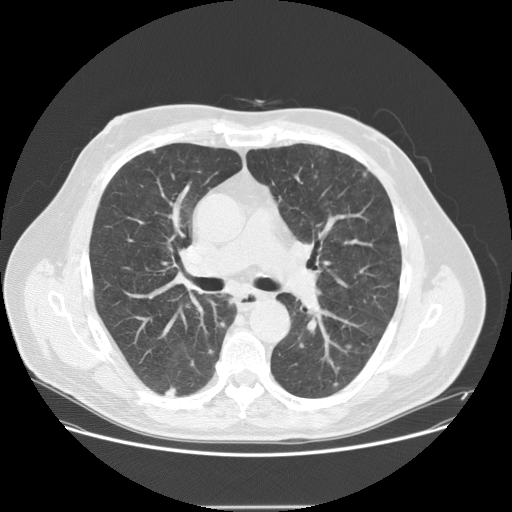
Low-dose screening chest CT, one axial slice. Slice 87 of 143 in the series (ordered by position). Reconstruction kernel STANDARD. Lung window (W 1500 / L -600 HU). 512 × 512 image matrix.
Structures marked on this image (manually delineated by an expert):
- lesion 3 (tumor, lower lobe of right lung): box from (x=165, y=386) to (x=177, y=398) px